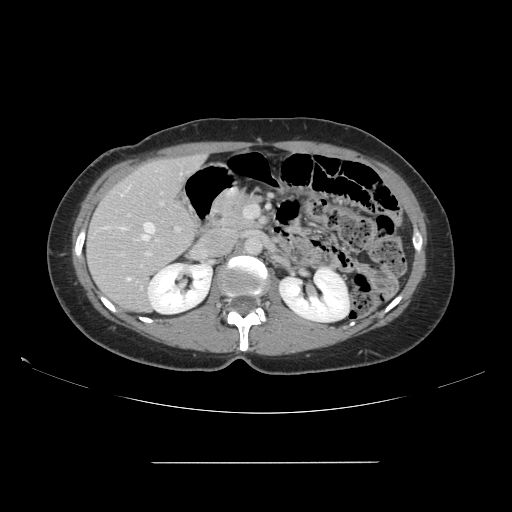
Contrast-enhanced abdominal CT, one axial slice. Slice 81 of 151 in the series (ordered by position). Intravenous contrast given. Soft-tissue window (W 400 / L 40 HU). 2.5 mm slice thickness. 512 × 512 image matrix, field of view 421 × 421 mm. Female patient, age 46 years. From the clinical record (not read from this slice): diagnosis: colorectal cancer liver metastases, imaged before liver resection; multiple liver metastases: yes; largest metastasis: 3 cm; chemotherapy before resection: no.
Annotated regions visible in this slice (expert manual segmentation):
- hepatic veins: bounding box <120,185,156,280> (left, top, right, bottom; pixels)
- liver: <88,156,204,312>
- planned liver remnant (the part of the liver to remain after resection): <96,156,201,312>
- portal vein (with intrahepatic branches): <120,191,246,260>